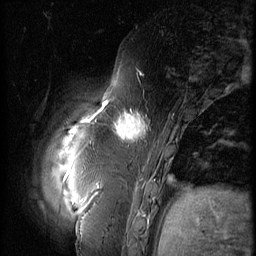
Breast MRI (dynamic contrast-enhanced), one sagittal slice; slice 10 of 60 in the series (ordered by position); 3 images stored at this slice position (order not interpretable as contrast timing); 1.5 T; TE 4.2 ms, TR 9 ms; 2.5 mm slice thickness; 256 × 256 image matrix, field of view 180 × 180 mm. Female patient, age 57 years. From the clinical record (not read from this slice): setting: breast cancer imaged before/during neoadjuvant chemotherapy; receptor status: triple-negative.
Annotated regions visible in this slice (semi-automatic segmentation, software-assisted and operator-edited):
- analysis volume of interest (the breast-tissue region the enhancement analysis was run in; not a lesion): bounding box (x1, y1, x2, y2) in pixels: (106, 101, 157, 152)
- tumour enhancement mask (voxels above the 140 % enhancement threshold inside the analysis volume of interest): (106, 102, 148, 139)